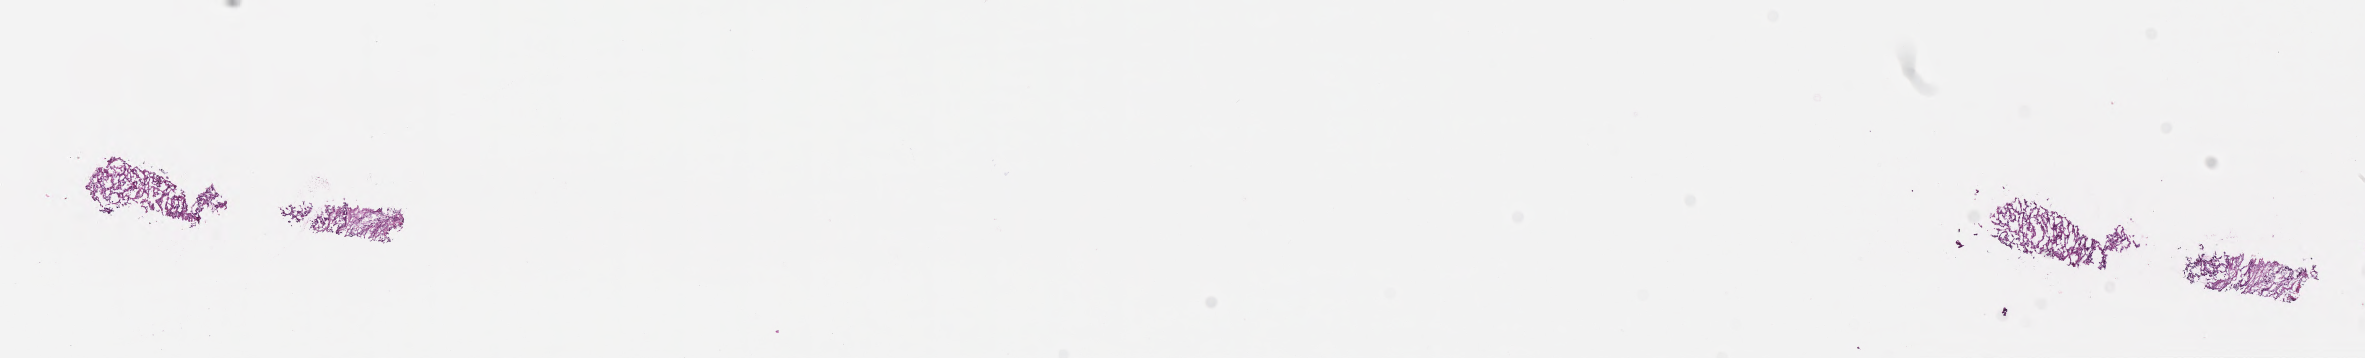
Haematoxylin and eosin whole-slide image — whole scanned area (about 19.1 x 2.9 mm) shown as a low-resolution overview; frozen section (tissue freezing medium); metastatic tumor tissue, resected from head of pancreas. Male, age 62 years at initial diagnosis. Composition of this section per pathologist review: tumor cells 80%, tumor nuclei 80%, stromal cells 20%, necrosis 0%, normal cells 0%. Inflammatory infiltration, as recorded: lymphocyte infiltration 0%, monocyte infiltration 0%, neutrophil infiltration 0%.
• section: top of the tissue portion
• patient diagnosis (primary): Infiltrating duct carcinoma, NOS